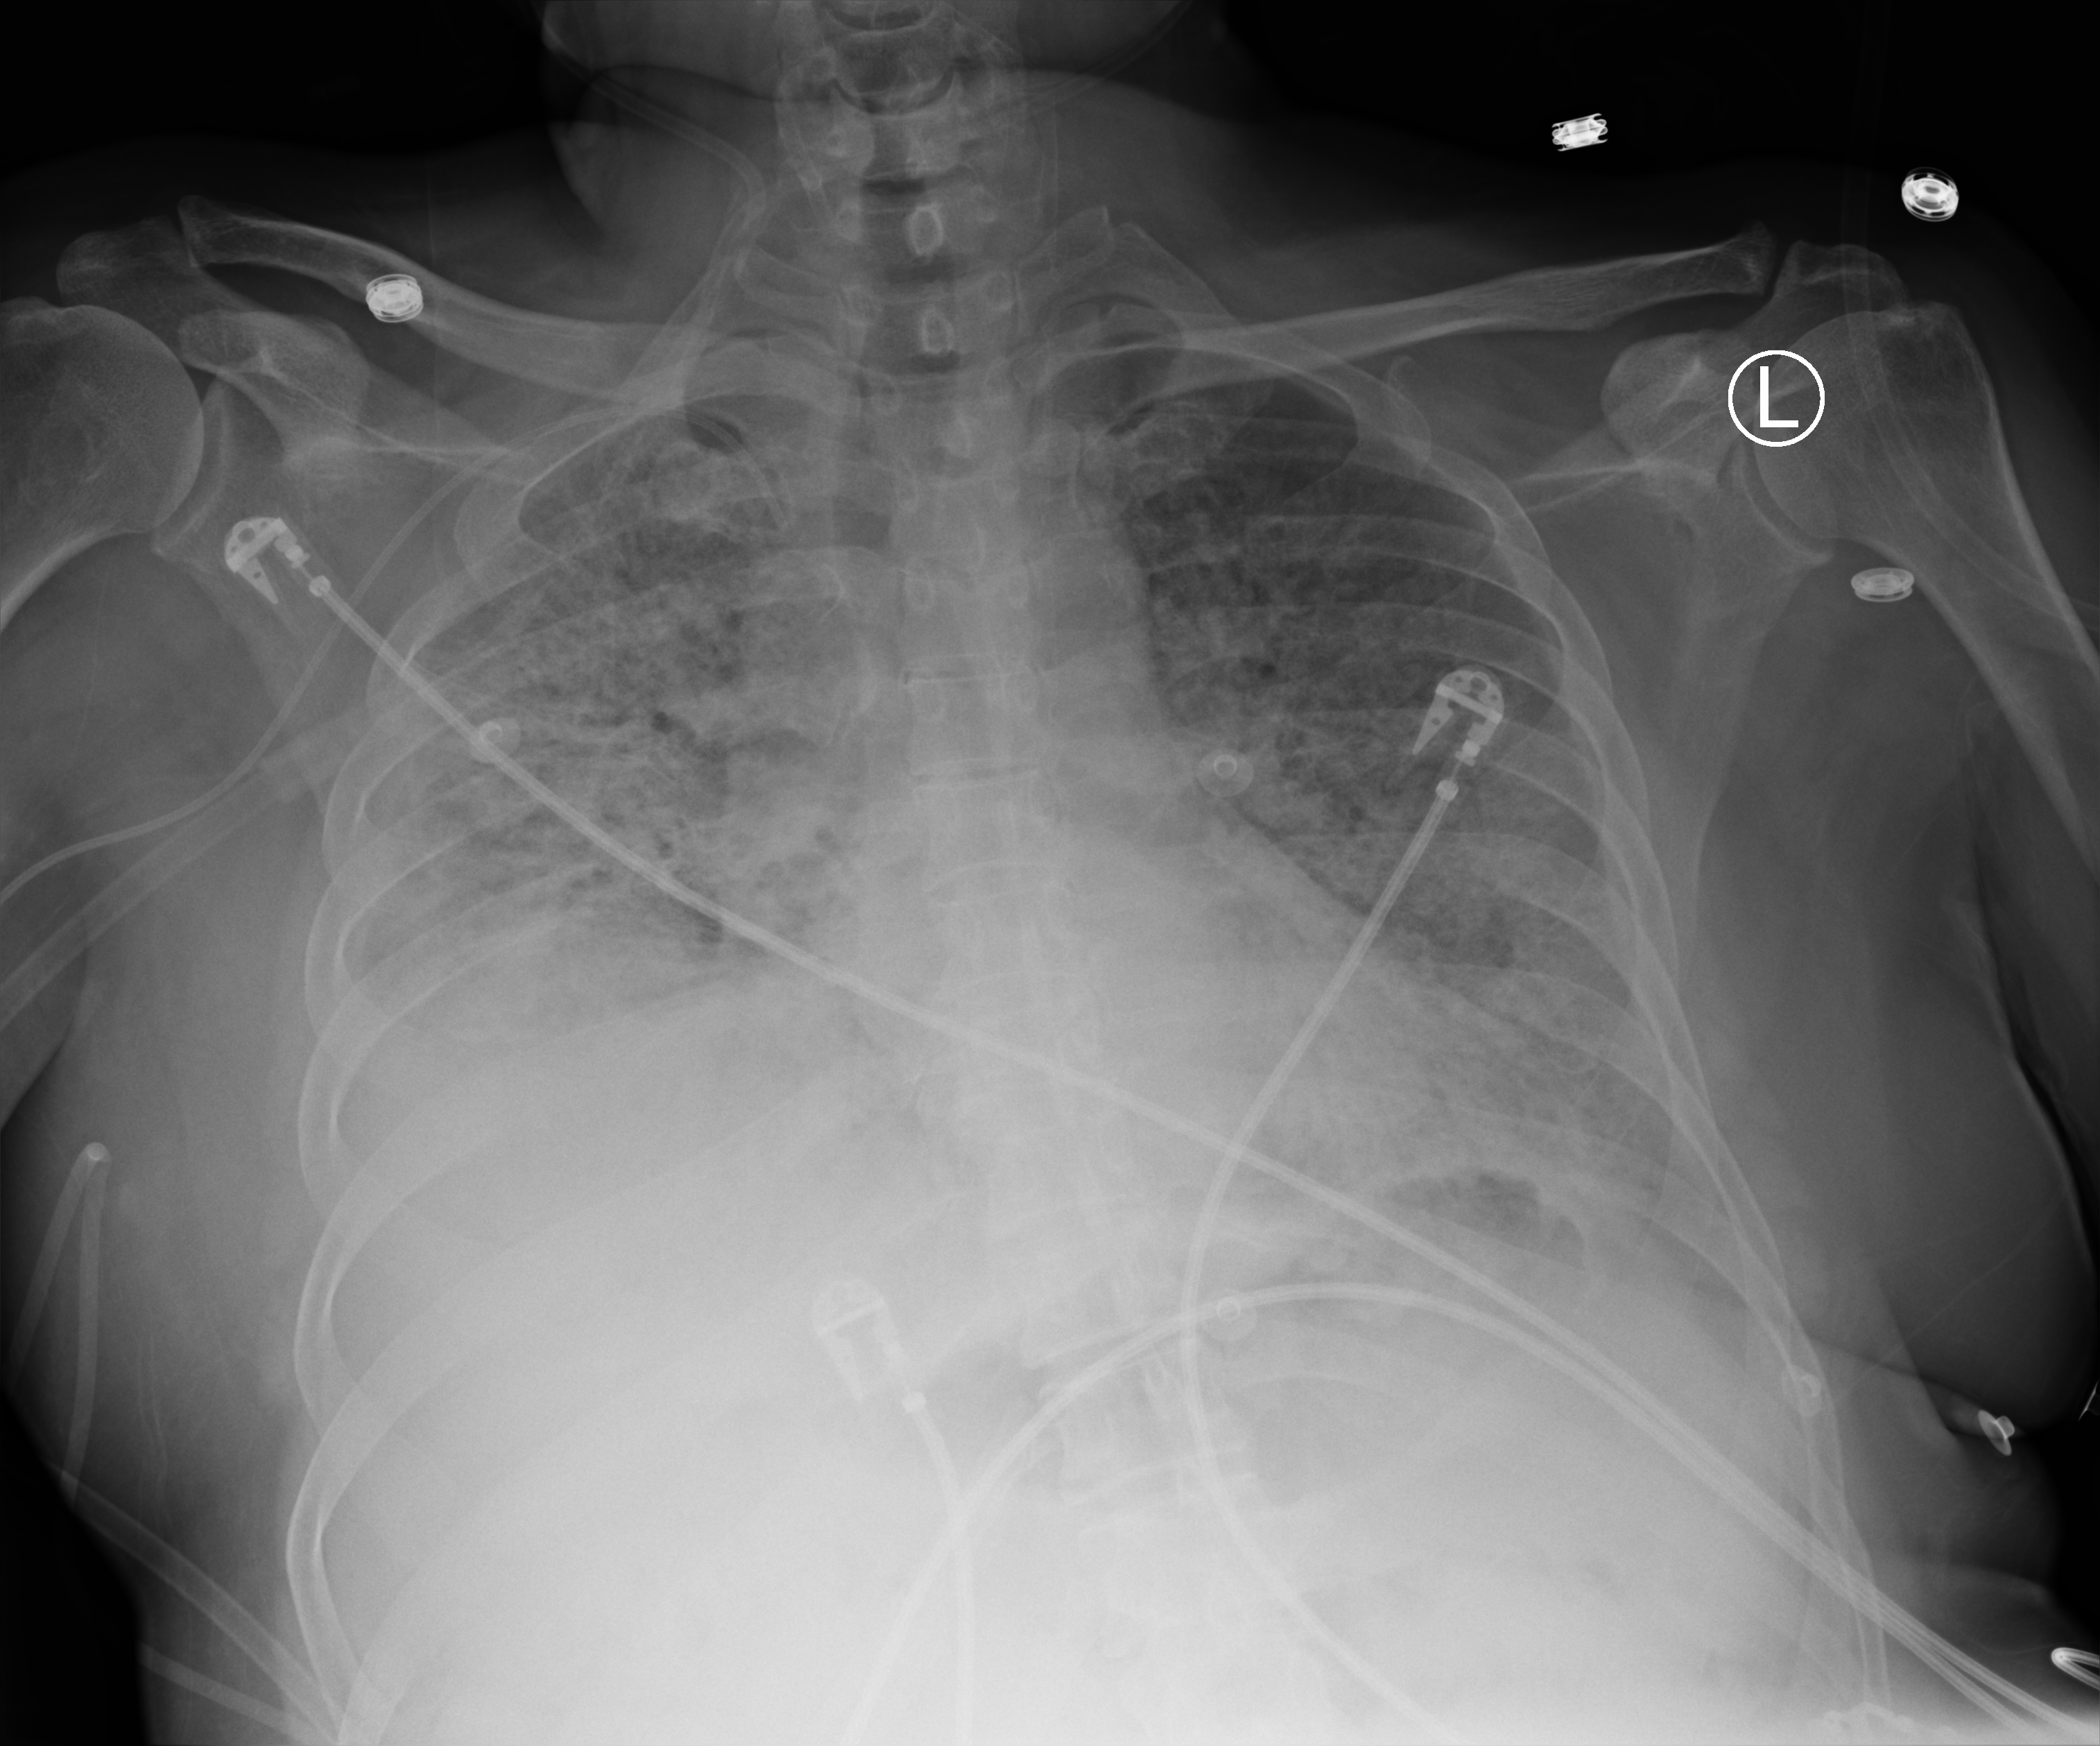
Portable chest radiograph; anteroposterior (AP) projection. Male patient hospitalised with COVID-19, age 18–59 years.
Admission-level facts for this patient (not findings on this image; timing relative to this image not recorded):
- admitted to intensive care during this hospital stay: yes
- length of hospital stay: 35 days
- COPD (admission record): no